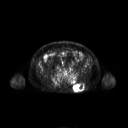
FDG PET of an extremity soft-tissue mass (from a PET/CT study), one axial slice; slice 87 of 267 in the series (ordered by position); 128 × 128 image matrix, field of view 700 × 700 mm. Patient: male, 61 years. From the clinical record (not read from this slice): histological type: pleiomorphic leiomyosarcoma; grade: high; site of the primary tumour: left buttock.
Outlined on this slice (expert contour drawn on MRI and transferred to this co-registered scan by the dataset authors):
- gross tumour volume including surrounding oedema: bounding box (x1, y1, x2, y2) in pixels: (73, 83, 84, 91)
- gross tumour volume (mass): (73, 84, 84, 91)